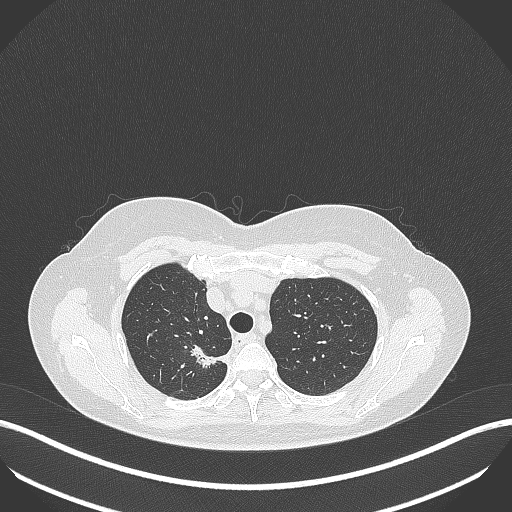
Chest CT, one axial slice; slice 312 of 386 in the series (ordered by position); lung window (W 1500 / L -600 HU); 1 mm slice thickness; 512 × 512 image matrix, field of view 400 × 400 mm. Female patient, age 65 years. Case-level facts recorded for this patient, not image findings: clinical TNM (as recorded): T1b N0 M0.
Structures marked on this image (rectangle marked by the reading radiologist):
- lung tumour (recorded histology: adenocarcinoma): bounding box (x1, y1, x2, y2) in pixels: (189, 342, 233, 373)